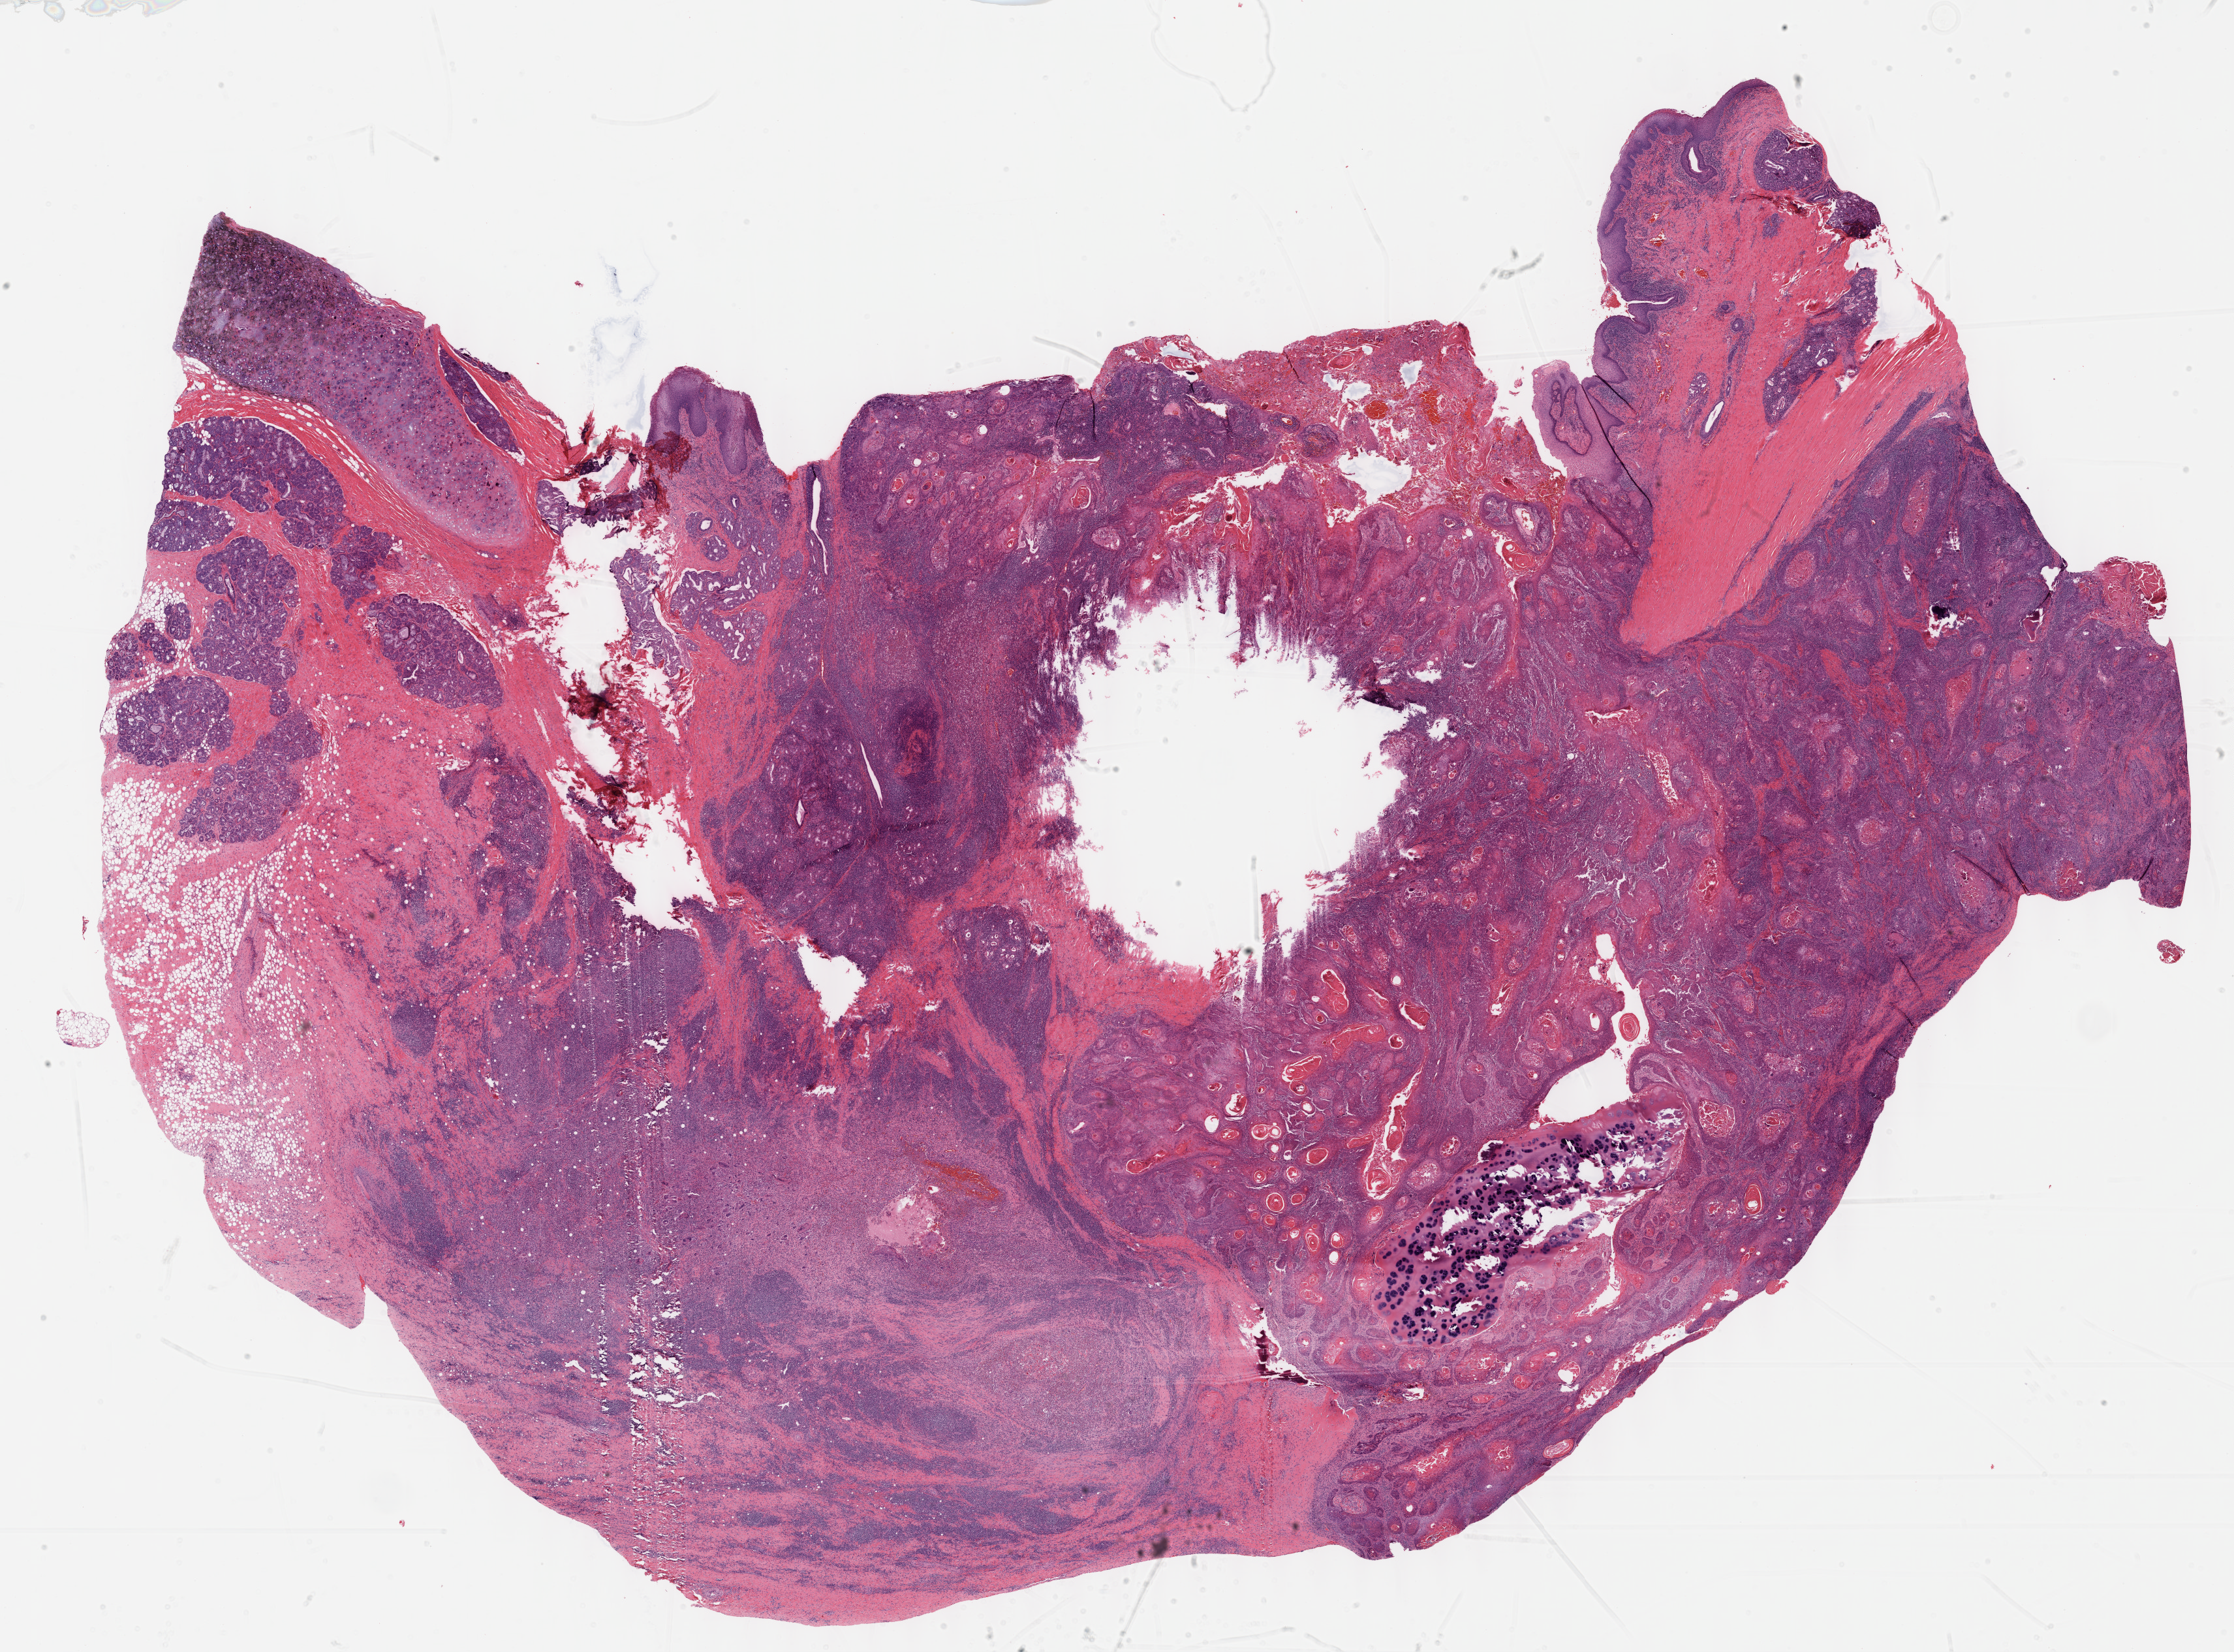
Digitized Hematoxylin and eosin (H&E) stained tissue section (whole slide), shown as a low-resolution overview of the whole scanned area (about 27.7 x 20.5 mm); formalin-fixed paraffin-embedded (FFPE) diagnostic section; primary tumour sample from the head and neck. Male patient; age at initial diagnosis 65 years.
Histologic diagnosis: Squamous cell carcinoma, NOS (larynx, NOS).